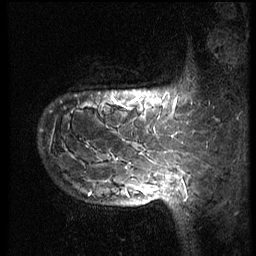
Breast MRI (dynamic contrast-enhanced), one sagittal slice; slice 15 of 66 in the series (ordered by position); 3 images stored at this slice position (order not interpretable as contrast timing); 1.5 T; TE 4.2 ms, TR 8.9 ms; 2.5 mm slice thickness; 256 × 256 image matrix, field of view 200 × 200 mm. Female patient, age 39 years. From the clinical record (not read from this slice): setting: breast cancer imaged before/during neoadjuvant chemotherapy; receptor status: HER2-positive.
Annotated regions visible in this slice (semi-automatic segmentation, software-assisted and operator-edited):
- analysis volume of interest (the breast-tissue region the enhancement analysis was run in; not a lesion): bounding box (x1, y1, x2, y2) in pixels: (38, 66, 166, 196)
- tumour enhancement mask (voxels above the 140 % enhancement threshold inside the analysis volume of interest): (112, 97, 120, 160)